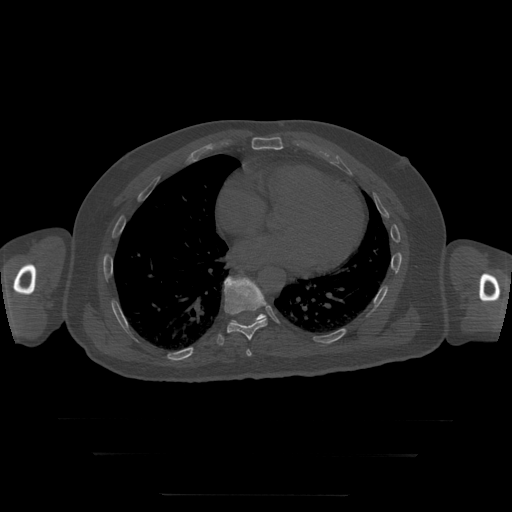
CT including the spine, one axial slice; slice 141 of 397 in the series (ordered by position); reconstruction kernel STANDARD; 120 kVp; bone window (W 1800 / L 400 HU); 1.25 mm slice thickness; 512 × 512 image matrix. Patient age 73 years. Case-level facts recorded for this patient, not image findings: primary cancer: prostate.
Outlined on this slice (semi-automatic segmentation, software-assisted and operator-edited):
- T10 vertebra: bounding box [x1, y1, x2, y2] px = [232, 314, 266, 324]
- T8 vertebra: [247, 350, 252, 356]
- T9 vertebra: [217, 278, 268, 346]